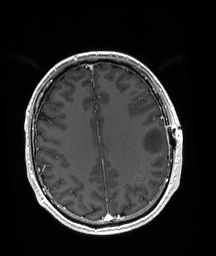
Brain MRI from a brain-tumour surgery series, one axial slice. Slice 70 of 192 in the series (ordered by position). T1-weighted post-contrast. 1 mm slice thickness. 216 × 256 image matrix. Case-level facts recorded for this patient, not image findings: histopathology: Astrocytoma; WHO grade: 3; IDH mutation: yes; tumour location: Left Posterior Frontal.
Outlined on this slice (expert manual segmentation):
- tumour: box from (x=140, y=127) to (x=166, y=155) px